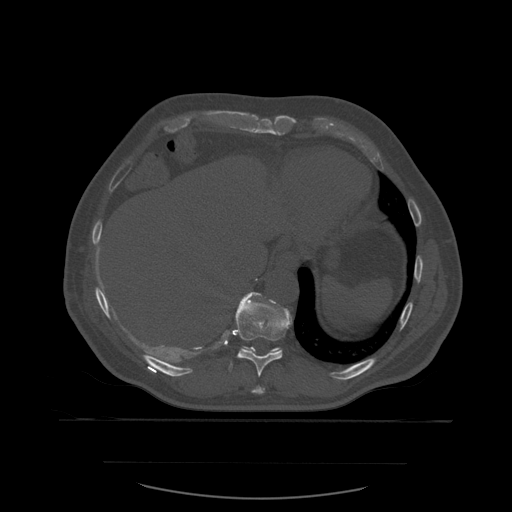
CT including the spine, one axial slice. Slice 315 of 590 in the series (ordered by position). Bone window (W 1800 / L 400 HU). 512 × 512 image matrix, field of view 479 × 479 mm. Patient age 71 years. From the clinical record (not read from this slice): primary cancer: lung; vertebrae with lytic lesions (as recorded): T1, T2, L5, S1.
Annotated regions visible in this slice (semi-automatic segmentation, software-assisted and operator-edited):
- T10 vertebra: box from (x=229, y=292) to (x=293, y=377) px
- T11 vertebra: (x=241, y=346)–(x=279, y=353)
- T9 vertebra: (x=252, y=386)–(x=265, y=394)